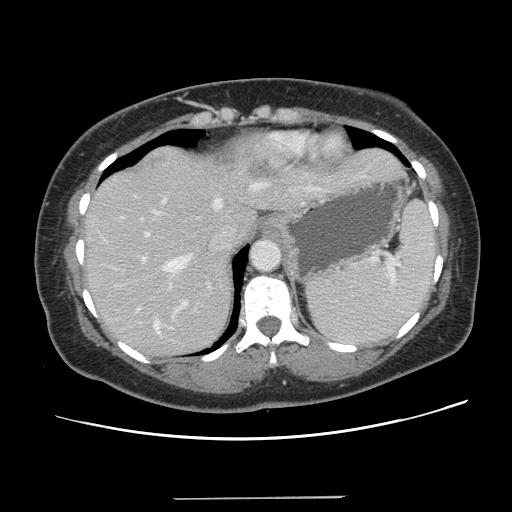
Contrast-enhanced abdominal CT, one axial slice. Slice 103 of 141 in the series (ordered by position). Intravenous contrast given. Soft-tissue window (W 400 / L 40 HU). 2.5 mm slice thickness. 512 × 512 image matrix, field of view 366 × 366 mm. Female patient, age 53 years. Case-level facts recorded for this patient, not image findings: diagnosis: colorectal cancer liver metastases, imaged before liver resection; multiple liver metastases: no; largest metastasis: 14.5 cm.
Outlined on this slice (outlined manually by an expert reader):
- hepatic veins: bounding box (x1, y1, x2, y2) in pixels: (153, 179, 271, 333)
- liver: (85, 146, 401, 358)
- planned liver remnant (the part of the liver to remain after resection): (85, 209, 258, 357)
- portal vein (with intrahepatic branches): (119, 188, 311, 320)